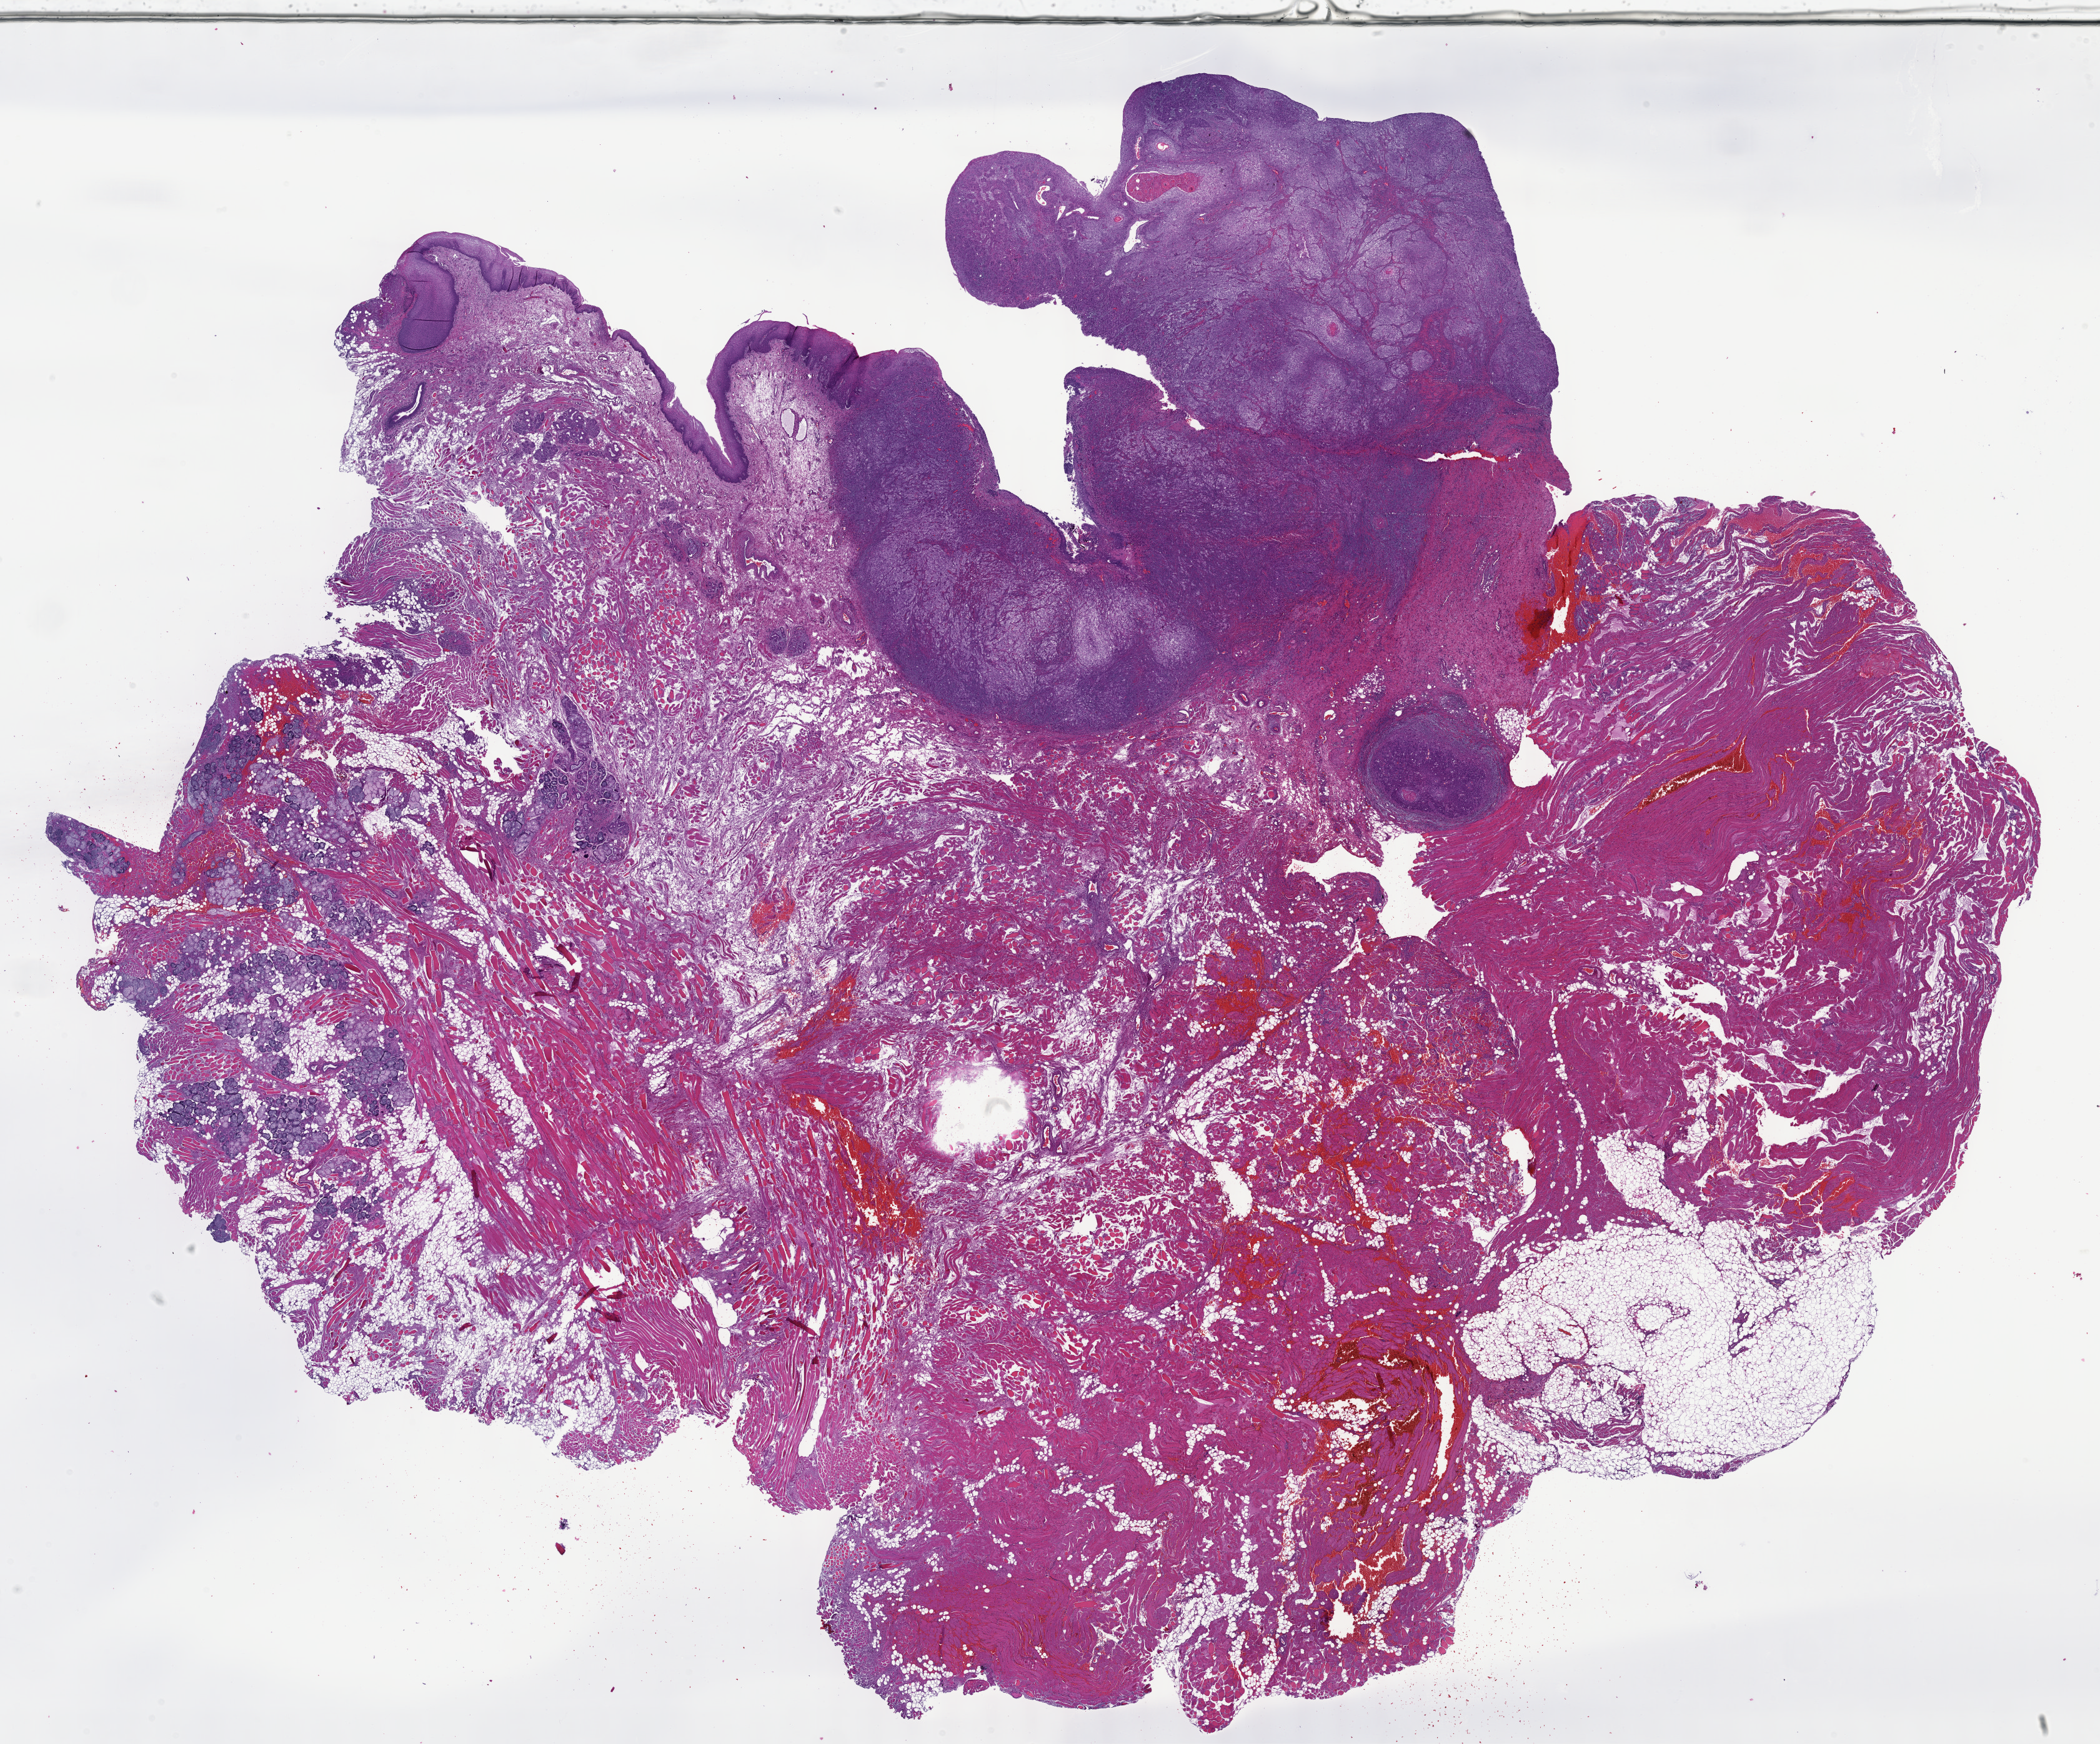
Digitized Hematoxylin and eosin (H&E) stained tissue section (whole slide), low-resolution overview of the scanned area, about 27.2 x 22.6 mm, formalin-fixed paraffin-embedded (FFPE) diagnostic section, primary tumour sample from the head and neck. Male, age 78 years at initial diagnosis.
Pathologic diagnosis: Squamous cell carcinoma, NOS (mouth, NOS).